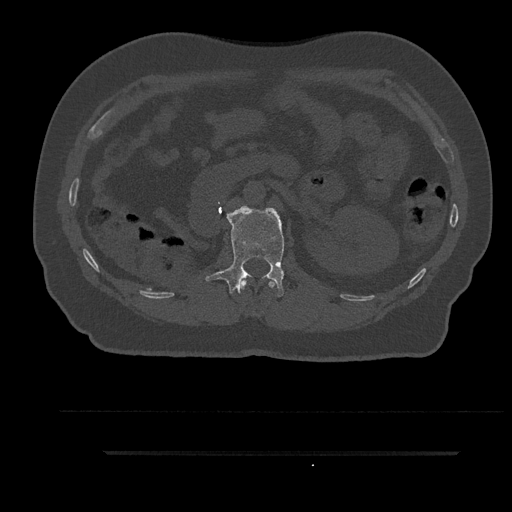
CT including the spine, one axial slice; slice 183 of 797 in the series (ordered by position); bone window (W 1800 / L 400 HU); 512 × 512 image matrix, field of view 432 × 432 mm. Male patient, age 63 years. Case-level facts recorded for this patient, not image findings: primary cancer: renal; vertebrae with lytic lesions (as recorded): T8.
Outlined on this slice (semi-automatically segmented with operator editing):
- L1 vertebra: bounding box [x1, y1, x2, y2] px = [205, 207, 285, 297]
- T12 vertebra: [240, 280, 276, 290]